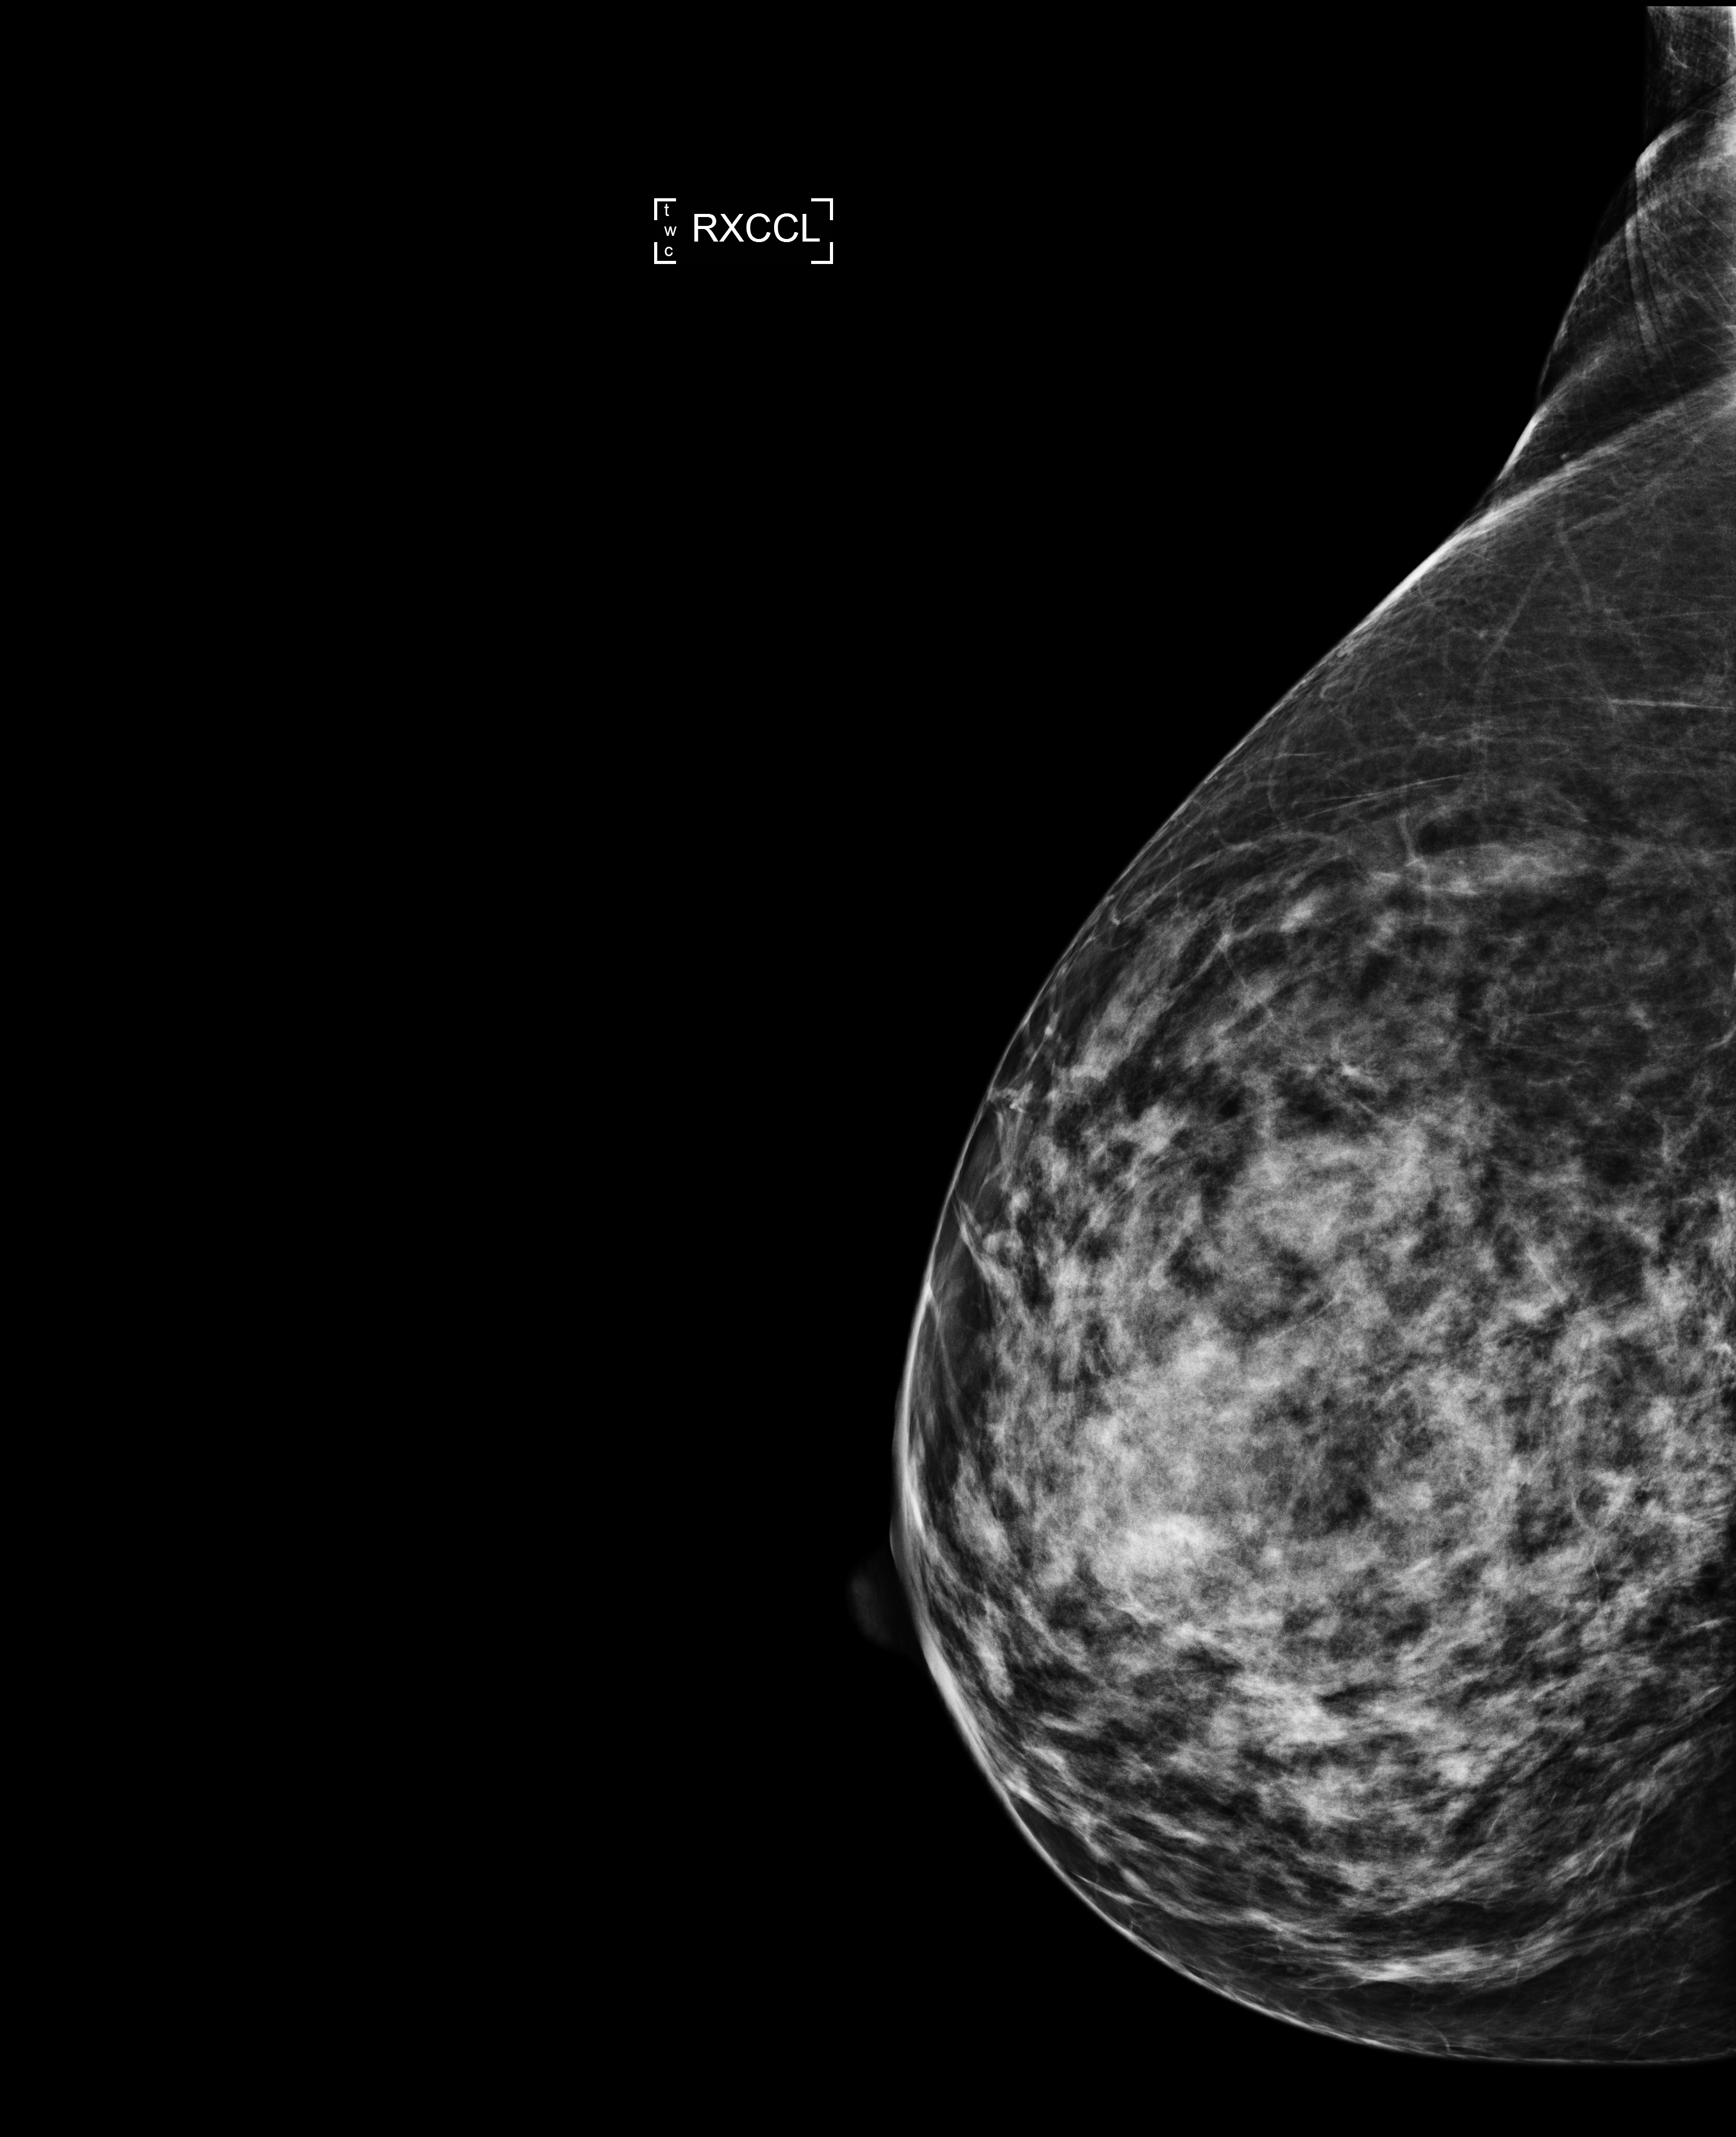
Digital mammogram (FFDM), right breast, exaggerated CC view (lateral), annual screening mammography examination. Patient: female, 44 years.
Breast density at the screening exam (both breasts): heterogeneously dense (BI-RADS density category c). Final BI-RADS assessment for this screening round (tomosynthesis exam, both breasts): category 2. Recall: no recall after this screen.